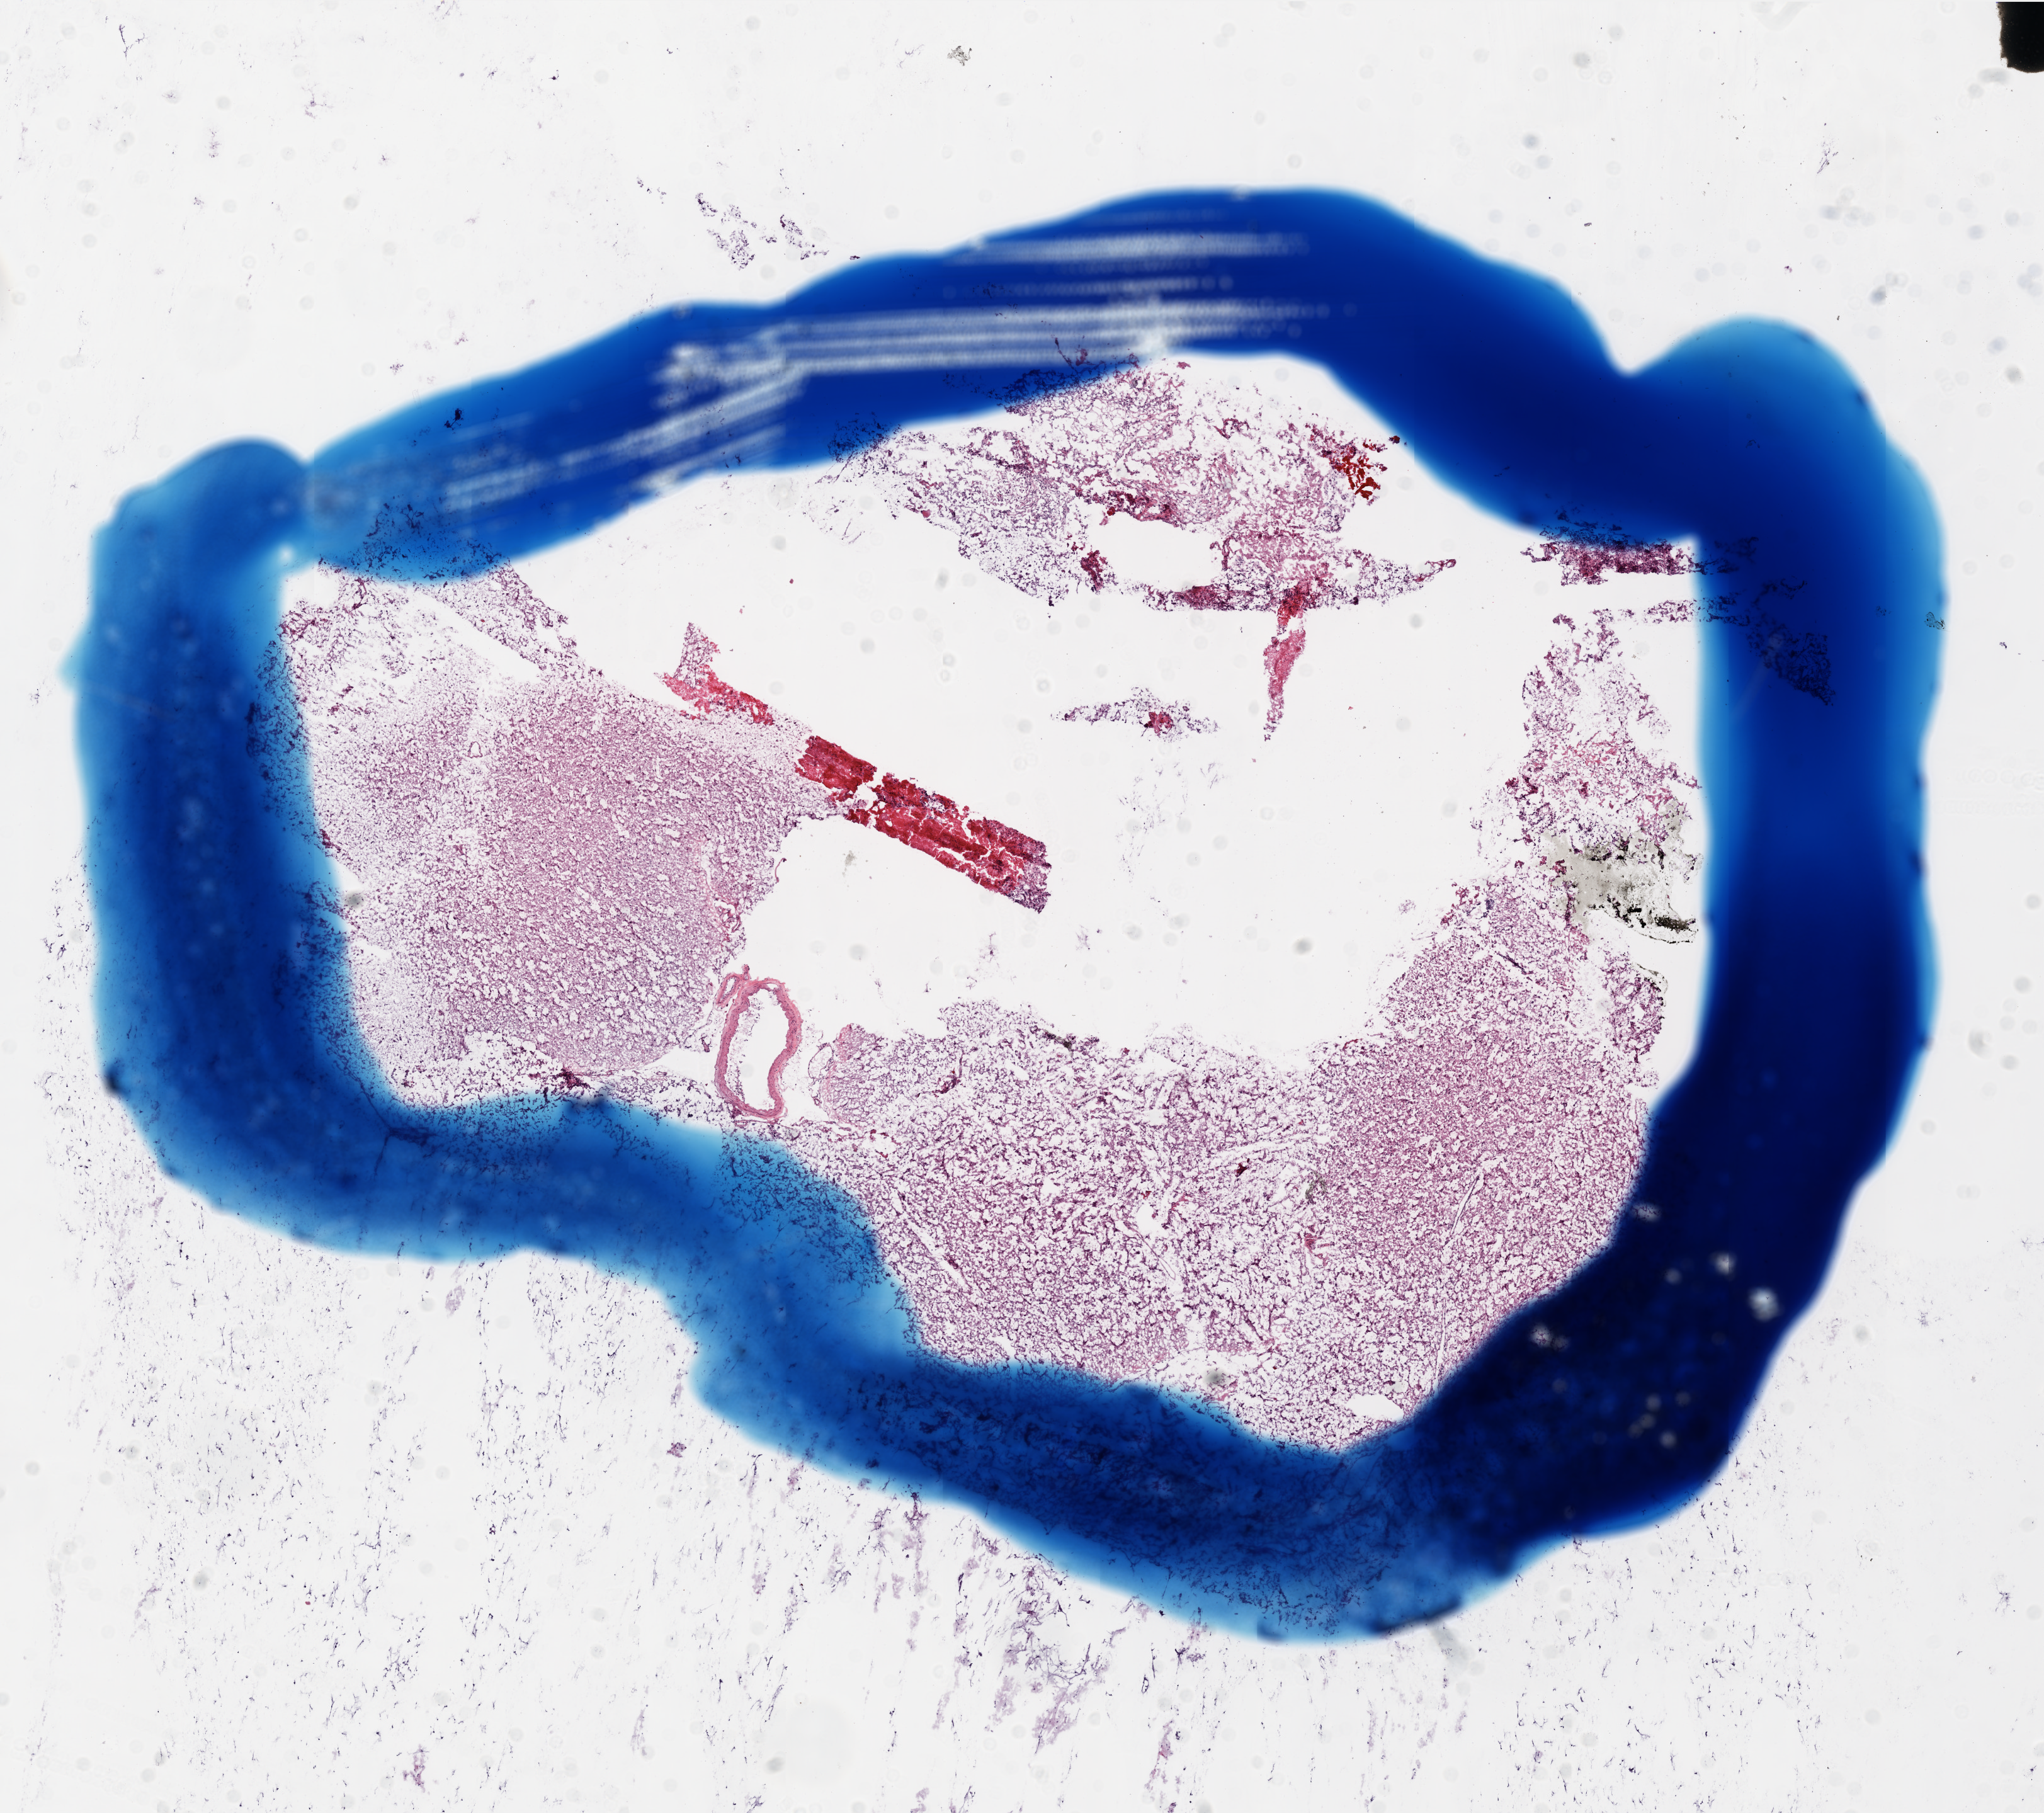
Whole-slide histology image, H&E — shown as a low-resolution overview of the whole scanned area (about 13.0 x 11.5 mm, acquisition: 20x scan). Frozen section from the top of the tissue portion. Brain, primary tumour sample. Patient: male, age at initial diagnosis 45 years. Slide review estimates, as recorded: tumour cells 0%, tumour nuclei 50%, normal cells 0%, stromal cells 90%, necrosis 10%.
Diagnosis: Glioblastoma.